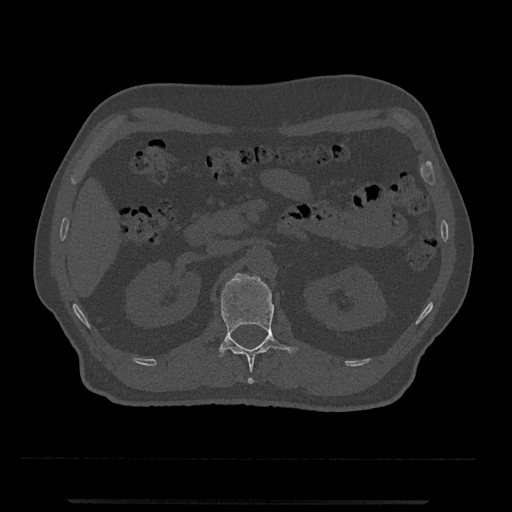
CT including the spine, one axial slice. Position 331 of 797 along the scan axis. Reconstruction kernel Br40s/3. 120 kVp. Bone window (W 1800 / L 400 HU). 512 × 512 image matrix. Male patient, age 63 years. From the clinical record (not read from this slice): primary cancer: prostate.
Structures marked on this image (semi-automatically segmented with operator editing):
- L1 vertebra: bounding box (x1, y1, x2, y2) in pixels: (218, 273, 298, 384)